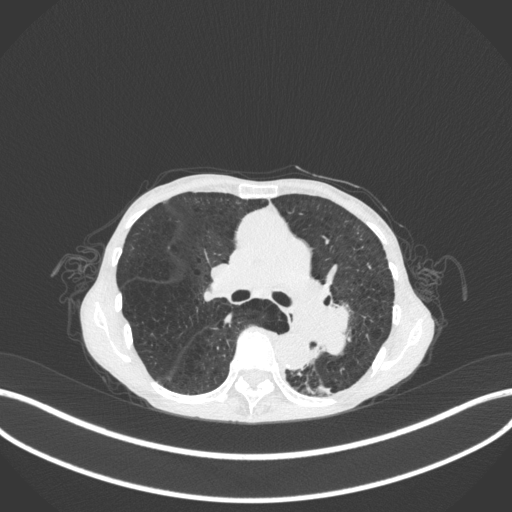
Chest CT, one axial slice; position 168 of 347 along the scan axis; reconstruction kernel B31f; 120 kVp; lung window (W 1500 / L -600 HU); 512 × 512 image matrix. Patient: female, 70 years. From the clinical record (not read from this slice): clinical TNM (as recorded): T3 N0 M0; histopathological grade: G3.
Structures marked on this image (rectangle marked by the reading radiologist):
- lung tumour (recorded histology: small cell carcinoma): bounding box (x1, y1, x2, y2) in pixels: (304, 290, 365, 361)